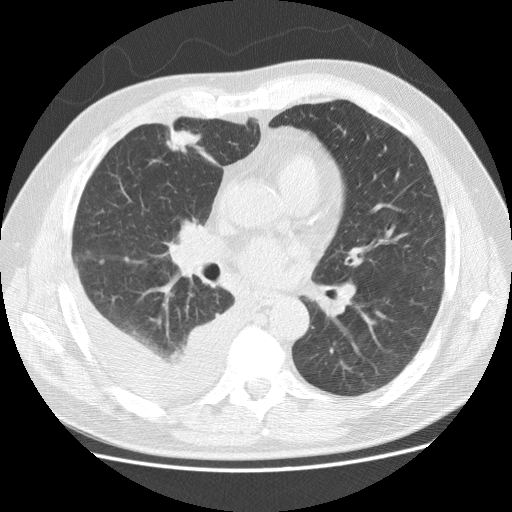
Low-dose screening chest CT, one axial slice; position 66 of 142 along the scan axis; lung window (W 1500 / L -600 HU); 512 × 512 image matrix.
Annotated regions visible in this slice (expert manual segmentation):
- lesion 1 (tumor, middle lobe of right lung): box from (x=166, y=128) to (x=201, y=152) px